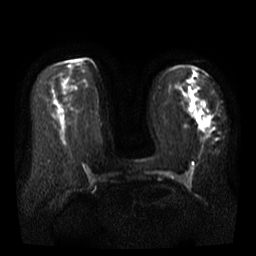
Breast MRI, one axial slice. Position 24 of 41 along the scan axis. Diffusion-weighted series; image 2 of 4 stored at this slice position (different b-values; order by instance number). 3 T. 5 mm slice thickness. 256 × 256 image matrix, field of view 340 × 340 mm. Female patient.
Structures marked on this image (expert manual segmentation):
- tumour on diffusion-weighted imaging: bounding box (x1, y1, x2, y2) in pixels: (195, 115, 210, 129)